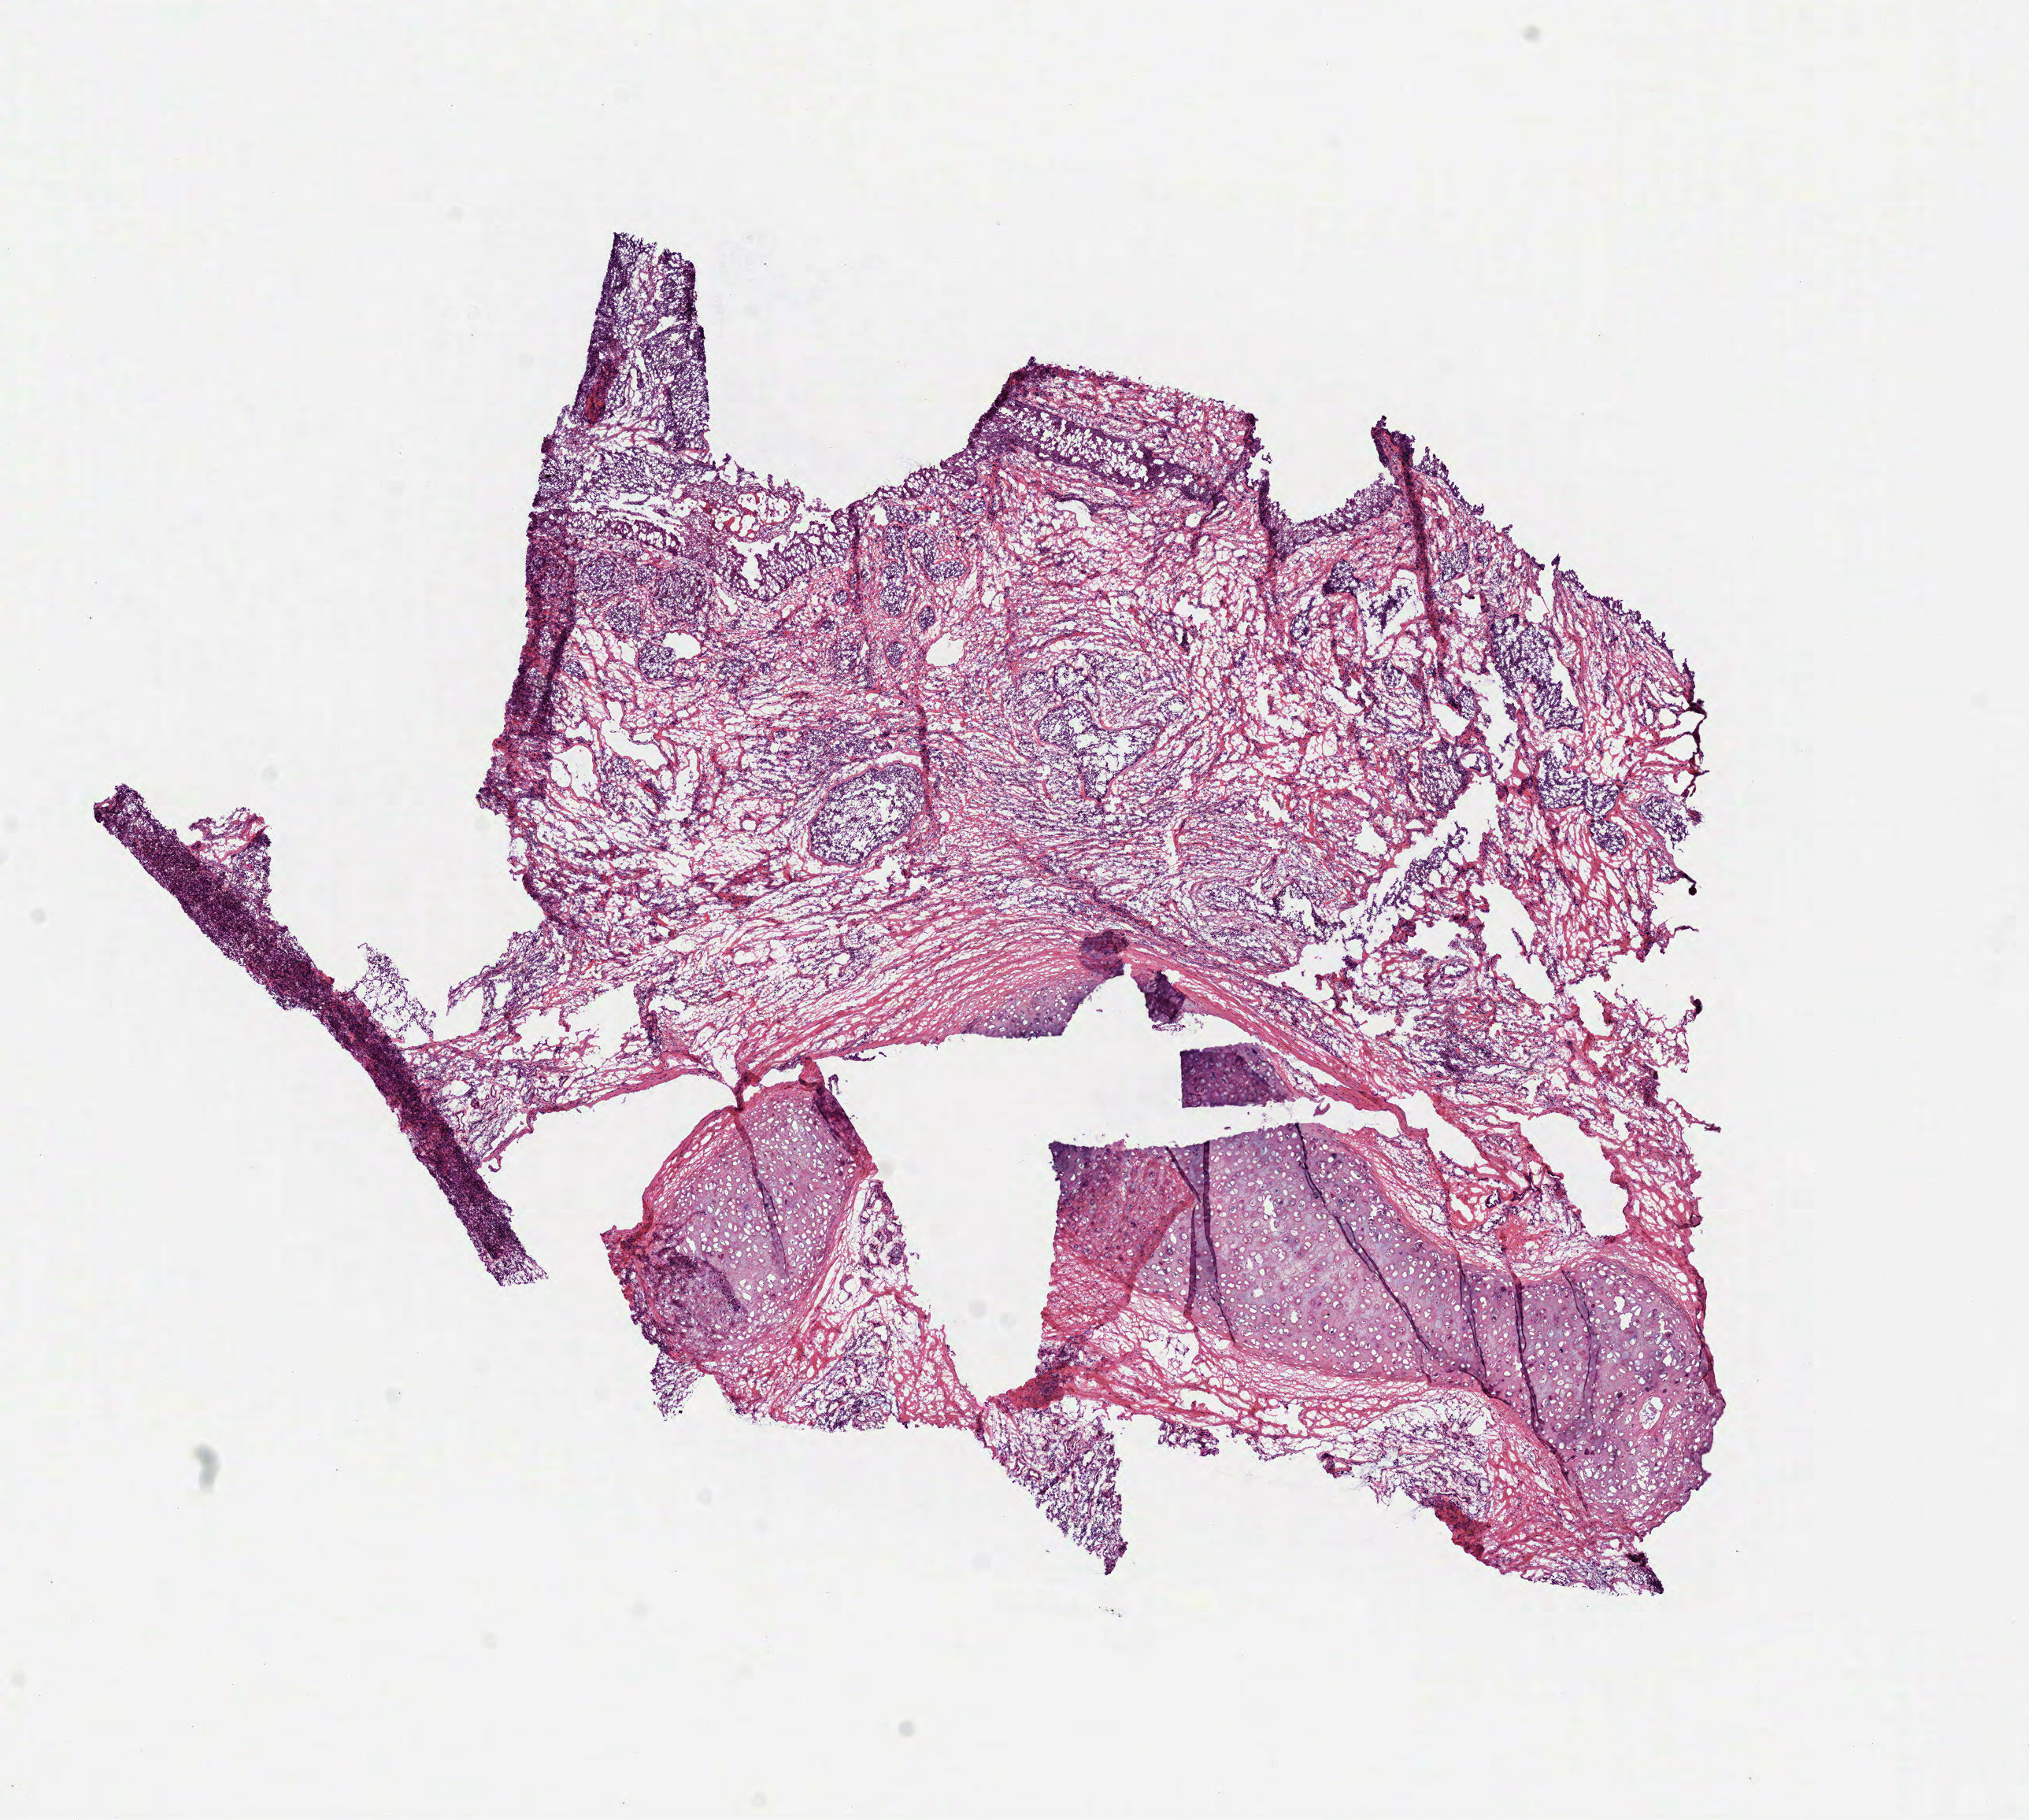
Hematoxylin and eosin (H&E) stained whole-slide image, low-resolution overview of the scanned area, about 10.4 x 9.3 mm (acquisition: 40x scan), frozen section from the top of the tissue portion, primary tumour sample from the head and neck. Male patient; age at initial diagnosis 60 years. Histologic grade: G3 (poorly differentiated). Pathologist review of this section (percent, as recorded): tumour cells 80%, tumour nuclei 80%, normal cells 20%, stromal cells 0%, necrosis 0%. Inflammatory infiltration, as recorded: lymphocyte infiltration 2%, monocyte infiltration 0%, neutrophil infiltration 0%.
* pathologic diagnosis: Squamous cell carcinoma, NOS (tongue, NOS)
* AJCC pathologic stage: IVA (7th edition)
* lymph nodes positive (case pathology): 2 of 12 examined